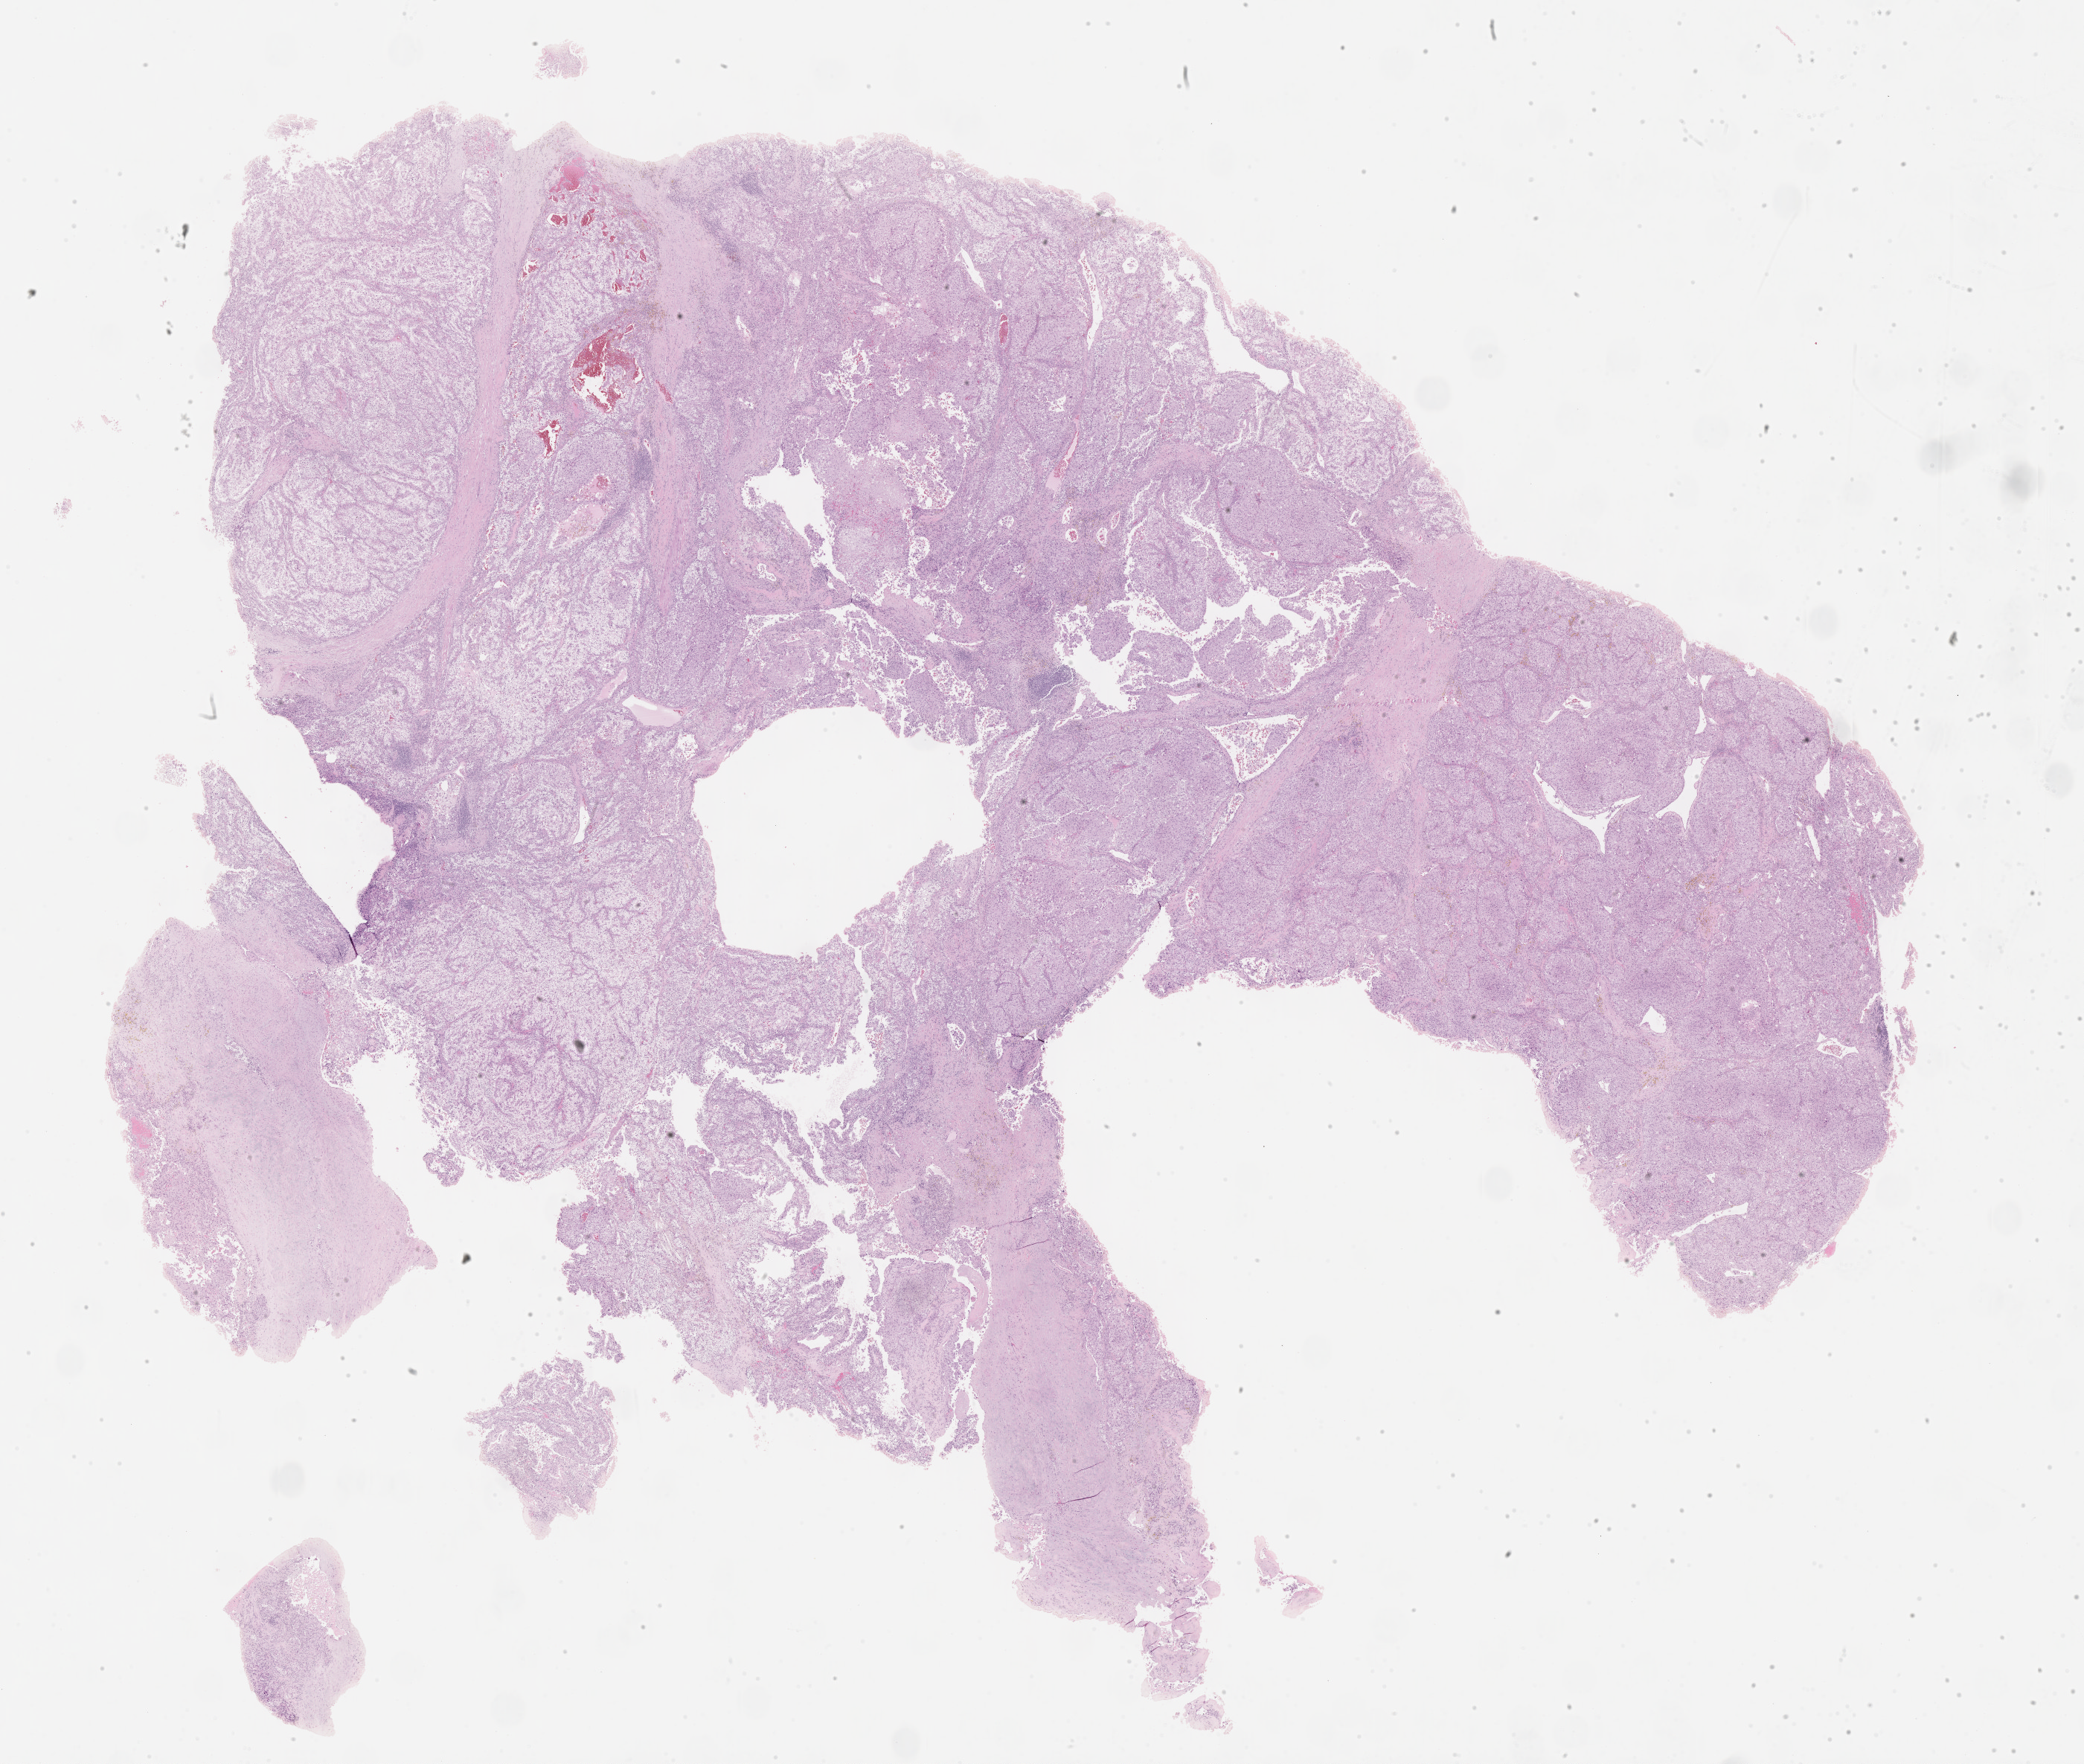
Whole-slide histology image, H&E, shown as a low-resolution overview of the whole scanned area (about 22.6 x 19.2 mm, from a 40x scan); FFPE section; sample: primary tumour, kidney. Patient: male, age at initial diagnosis 51 years.
Diagnosis: Clear cell adenocarcinoma, NOS.